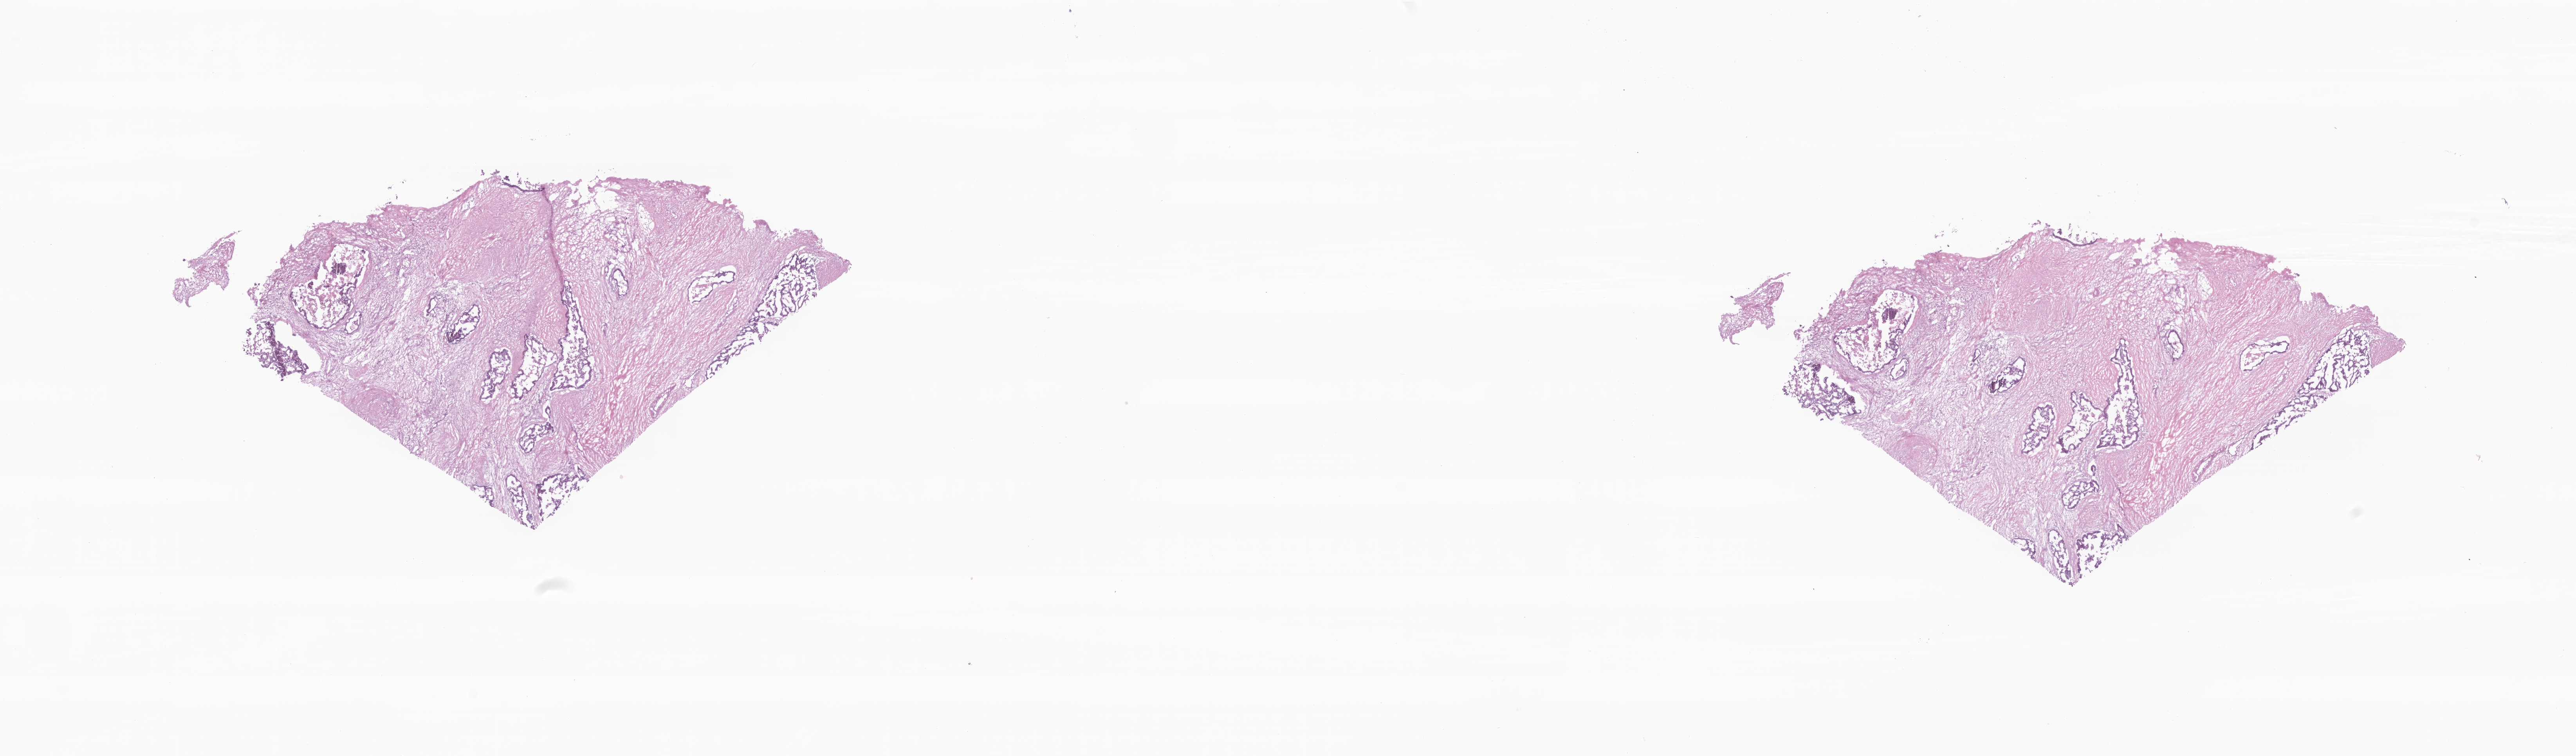
Digitized haematoxylin and eosin-stained section, shown as a low-resolution overview of the whole scanned area (about 27.7 x 8.1 mm); frozen section; metastatic tumor tissue, resected from liver. Male patient; age at initial diagnosis 70 years. Composition of this section per pathologist review: tumor cells 80%, tumor nuclei 80%, stromal cells 15%, necrosis 5%, normal cells 0%. Infiltration values recorded for this section: lymphocyte infiltration 3%, monocyte infiltration 1%, neutrophil infiltration 6%.
Patient diagnosis (primary): Adenocarcinoma, NOS.